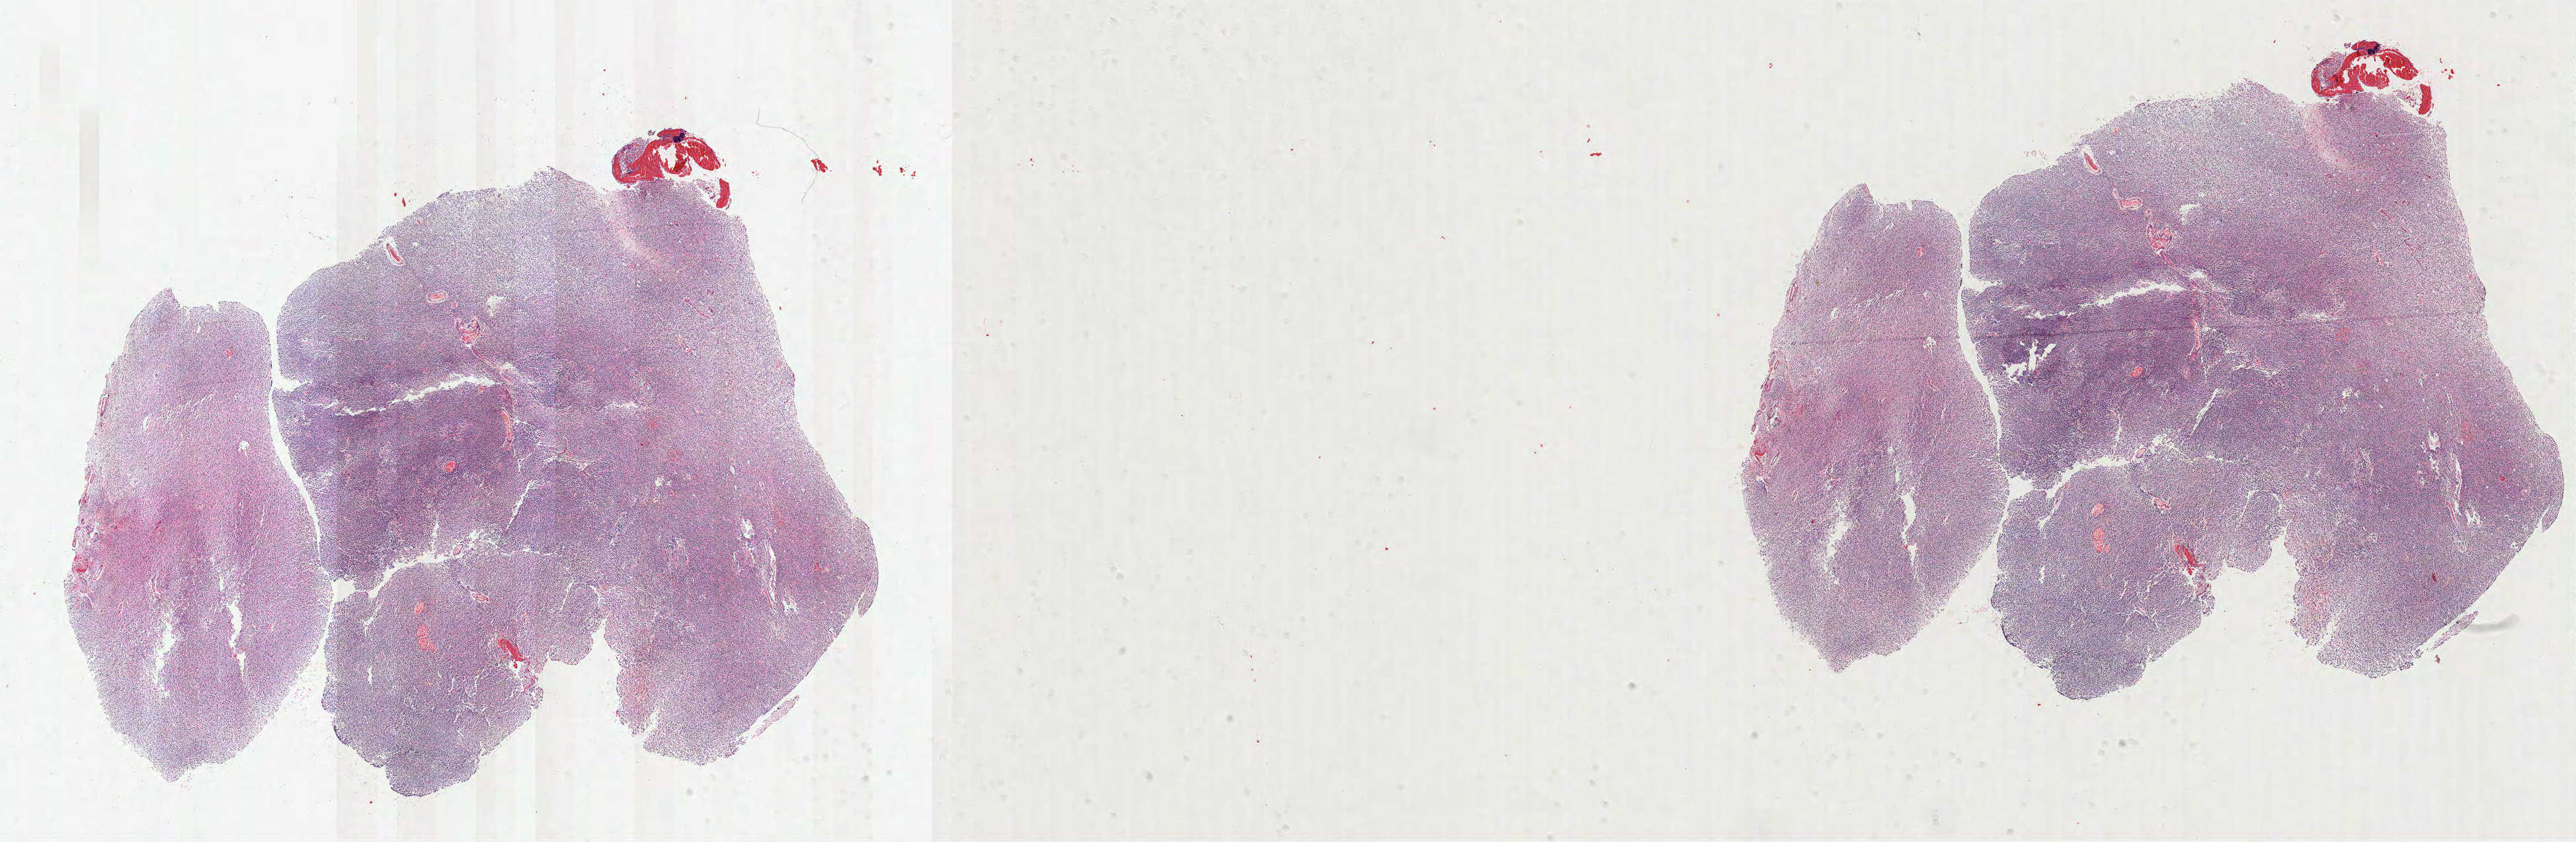
H&E whole-slide image — a low-resolution overview of the entire scanned area, about 31.4 x 10.3 mm (from a 40x scan), formalin-fixed paraffin-embedded (FFPE) diagnostic section, primary tumour sample from the brain. Patient: female, age at initial diagnosis 47 years. Histologic grade: G2 (moderately differentiated).
Histologic diagnosis: Oligodendroglioma, NOS (cerebrum). Laterality: right.